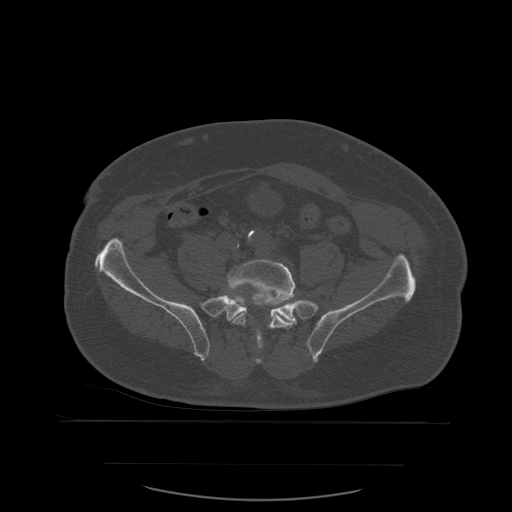
CT including the spine, one axial slice. Slice 128 of 590 in the series (ordered by position). Bone window (W 1800 / L 400 HU). 1.25 mm slice thickness. 512 × 512 image matrix. Patient age 71 years. From the clinical record (not read from this slice): primary cancer: lung; vertebrae with lytic lesions (as recorded): T1, T2, L5, S1.
Annotated regions visible in this slice (semi-automatic segmentation, software-assisted and operator-edited):
- L5 vertebra: bounding box [x1, y1, x2, y2] px = [224, 260, 296, 351]